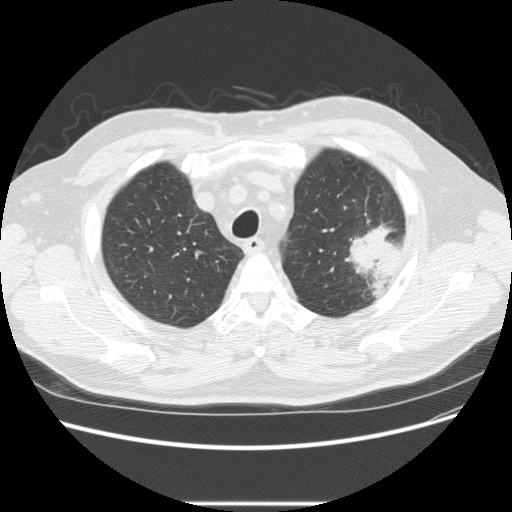
Low-dose screening chest CT, one axial slice; position 185 of 233 along the scan axis; 120 kVp; lung window (W 1500 / L -600 HU); 2.5 mm slice thickness; 512 × 512 image matrix, field of view 380 × 380 mm.
Structures marked on this image (manually delineated by an expert):
- lesion 1 (tumor, upper lobe of left lung): bounding box (x1, y1, x2, y2) in pixels: (345, 223, 402, 297)